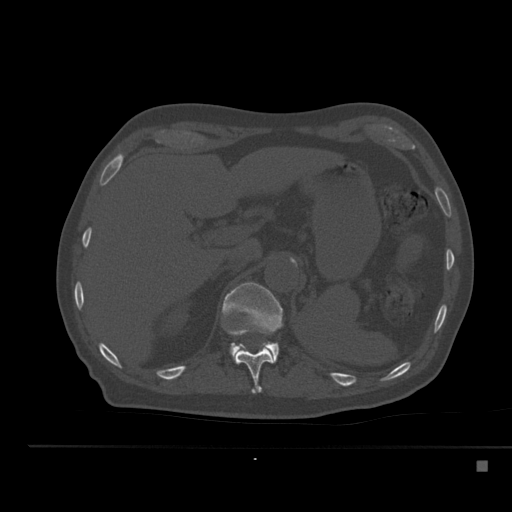
CT including the spine, one axial slice. Position 242 of 517 along the scan axis. Bone window (W 1800 / L 400 HU). 512 × 512 image matrix, field of view 408 × 408 mm. Male patient, age 70 years. From the clinical record (not read from this slice): primary cancer: renal; vertebrae with lytic lesions (as recorded): T4, T6, T10, T12, L3, L4, L5.
Outlined on this slice (semi-automatically segmented with operator editing):
- T11 vertebra: bounding box <227,329,273,394> (left, top, right, bottom; pixels)
- T12 vertebra: <222,282,283,364>